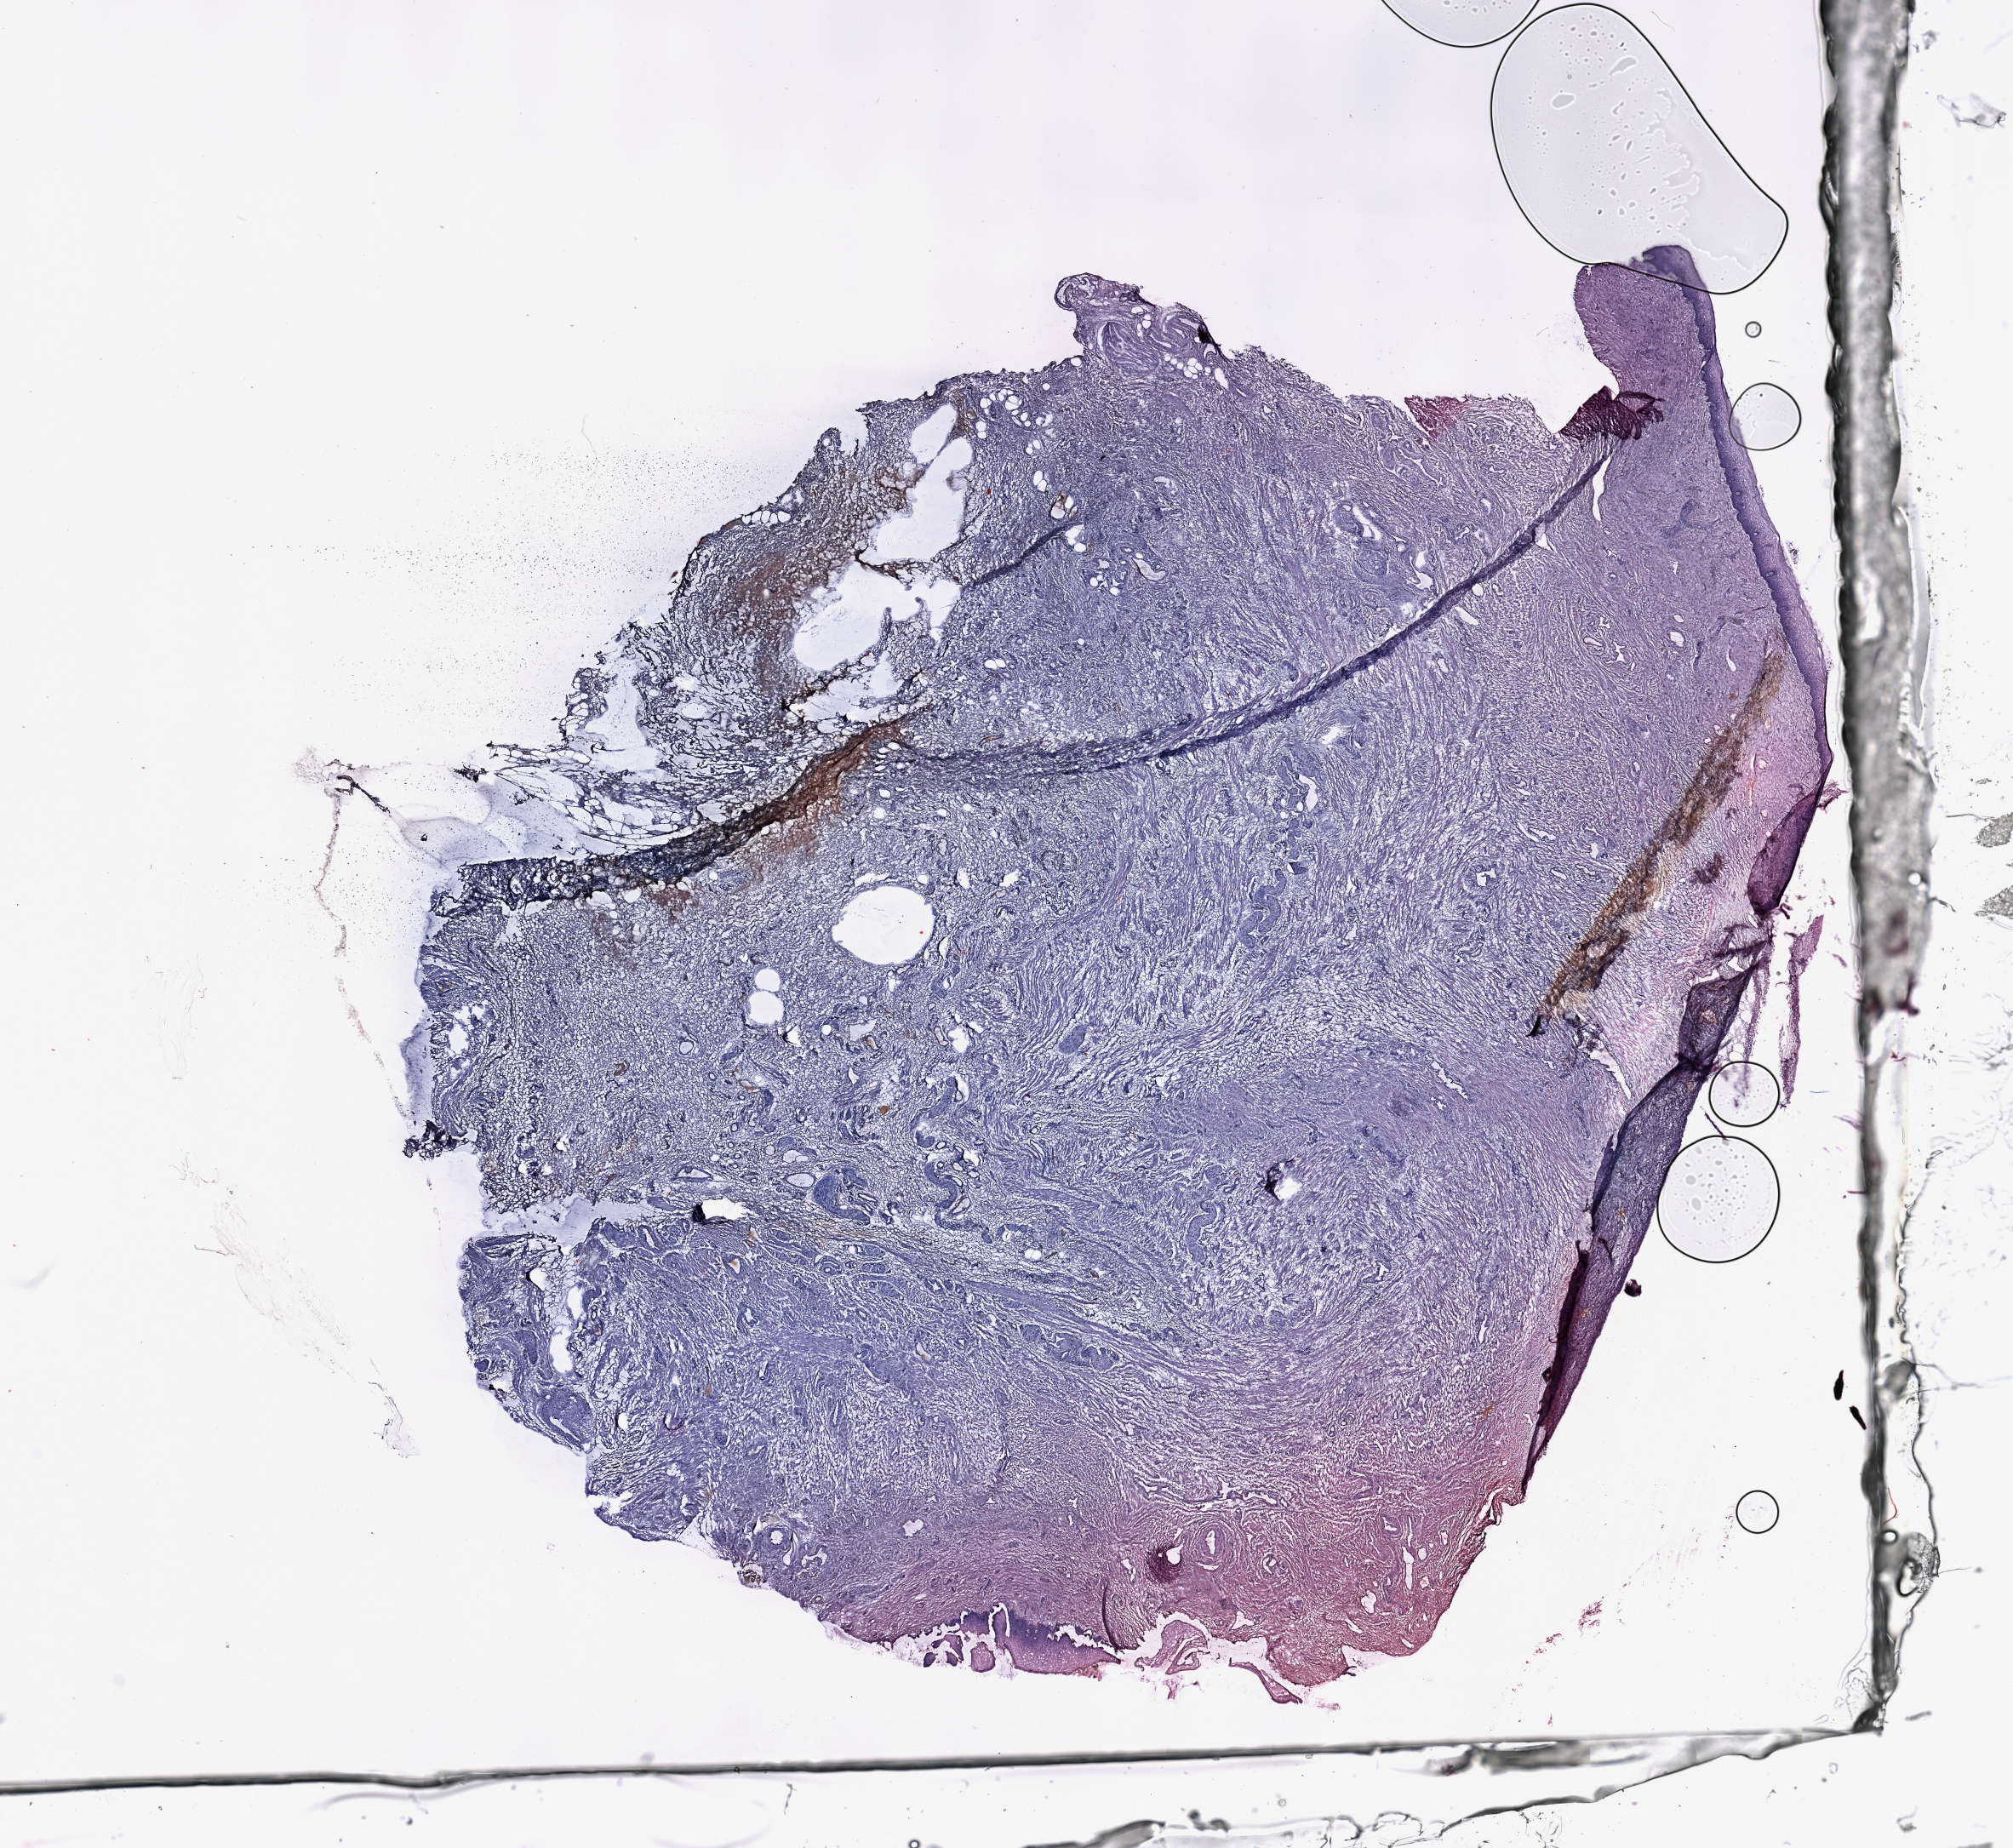
Hematoxylin and eosin (H&E) stained whole-slide image — whole scanned area (about 18.7 x 17.2 mm) shown as a low-resolution overview. Uterus, normal (non-tumour) tissue. Female, 41 y/o.
• this section: normal (non-tumour) tissue from the same patient
• patient diagnosis: Endometrioid adenocarcinoma, NOS